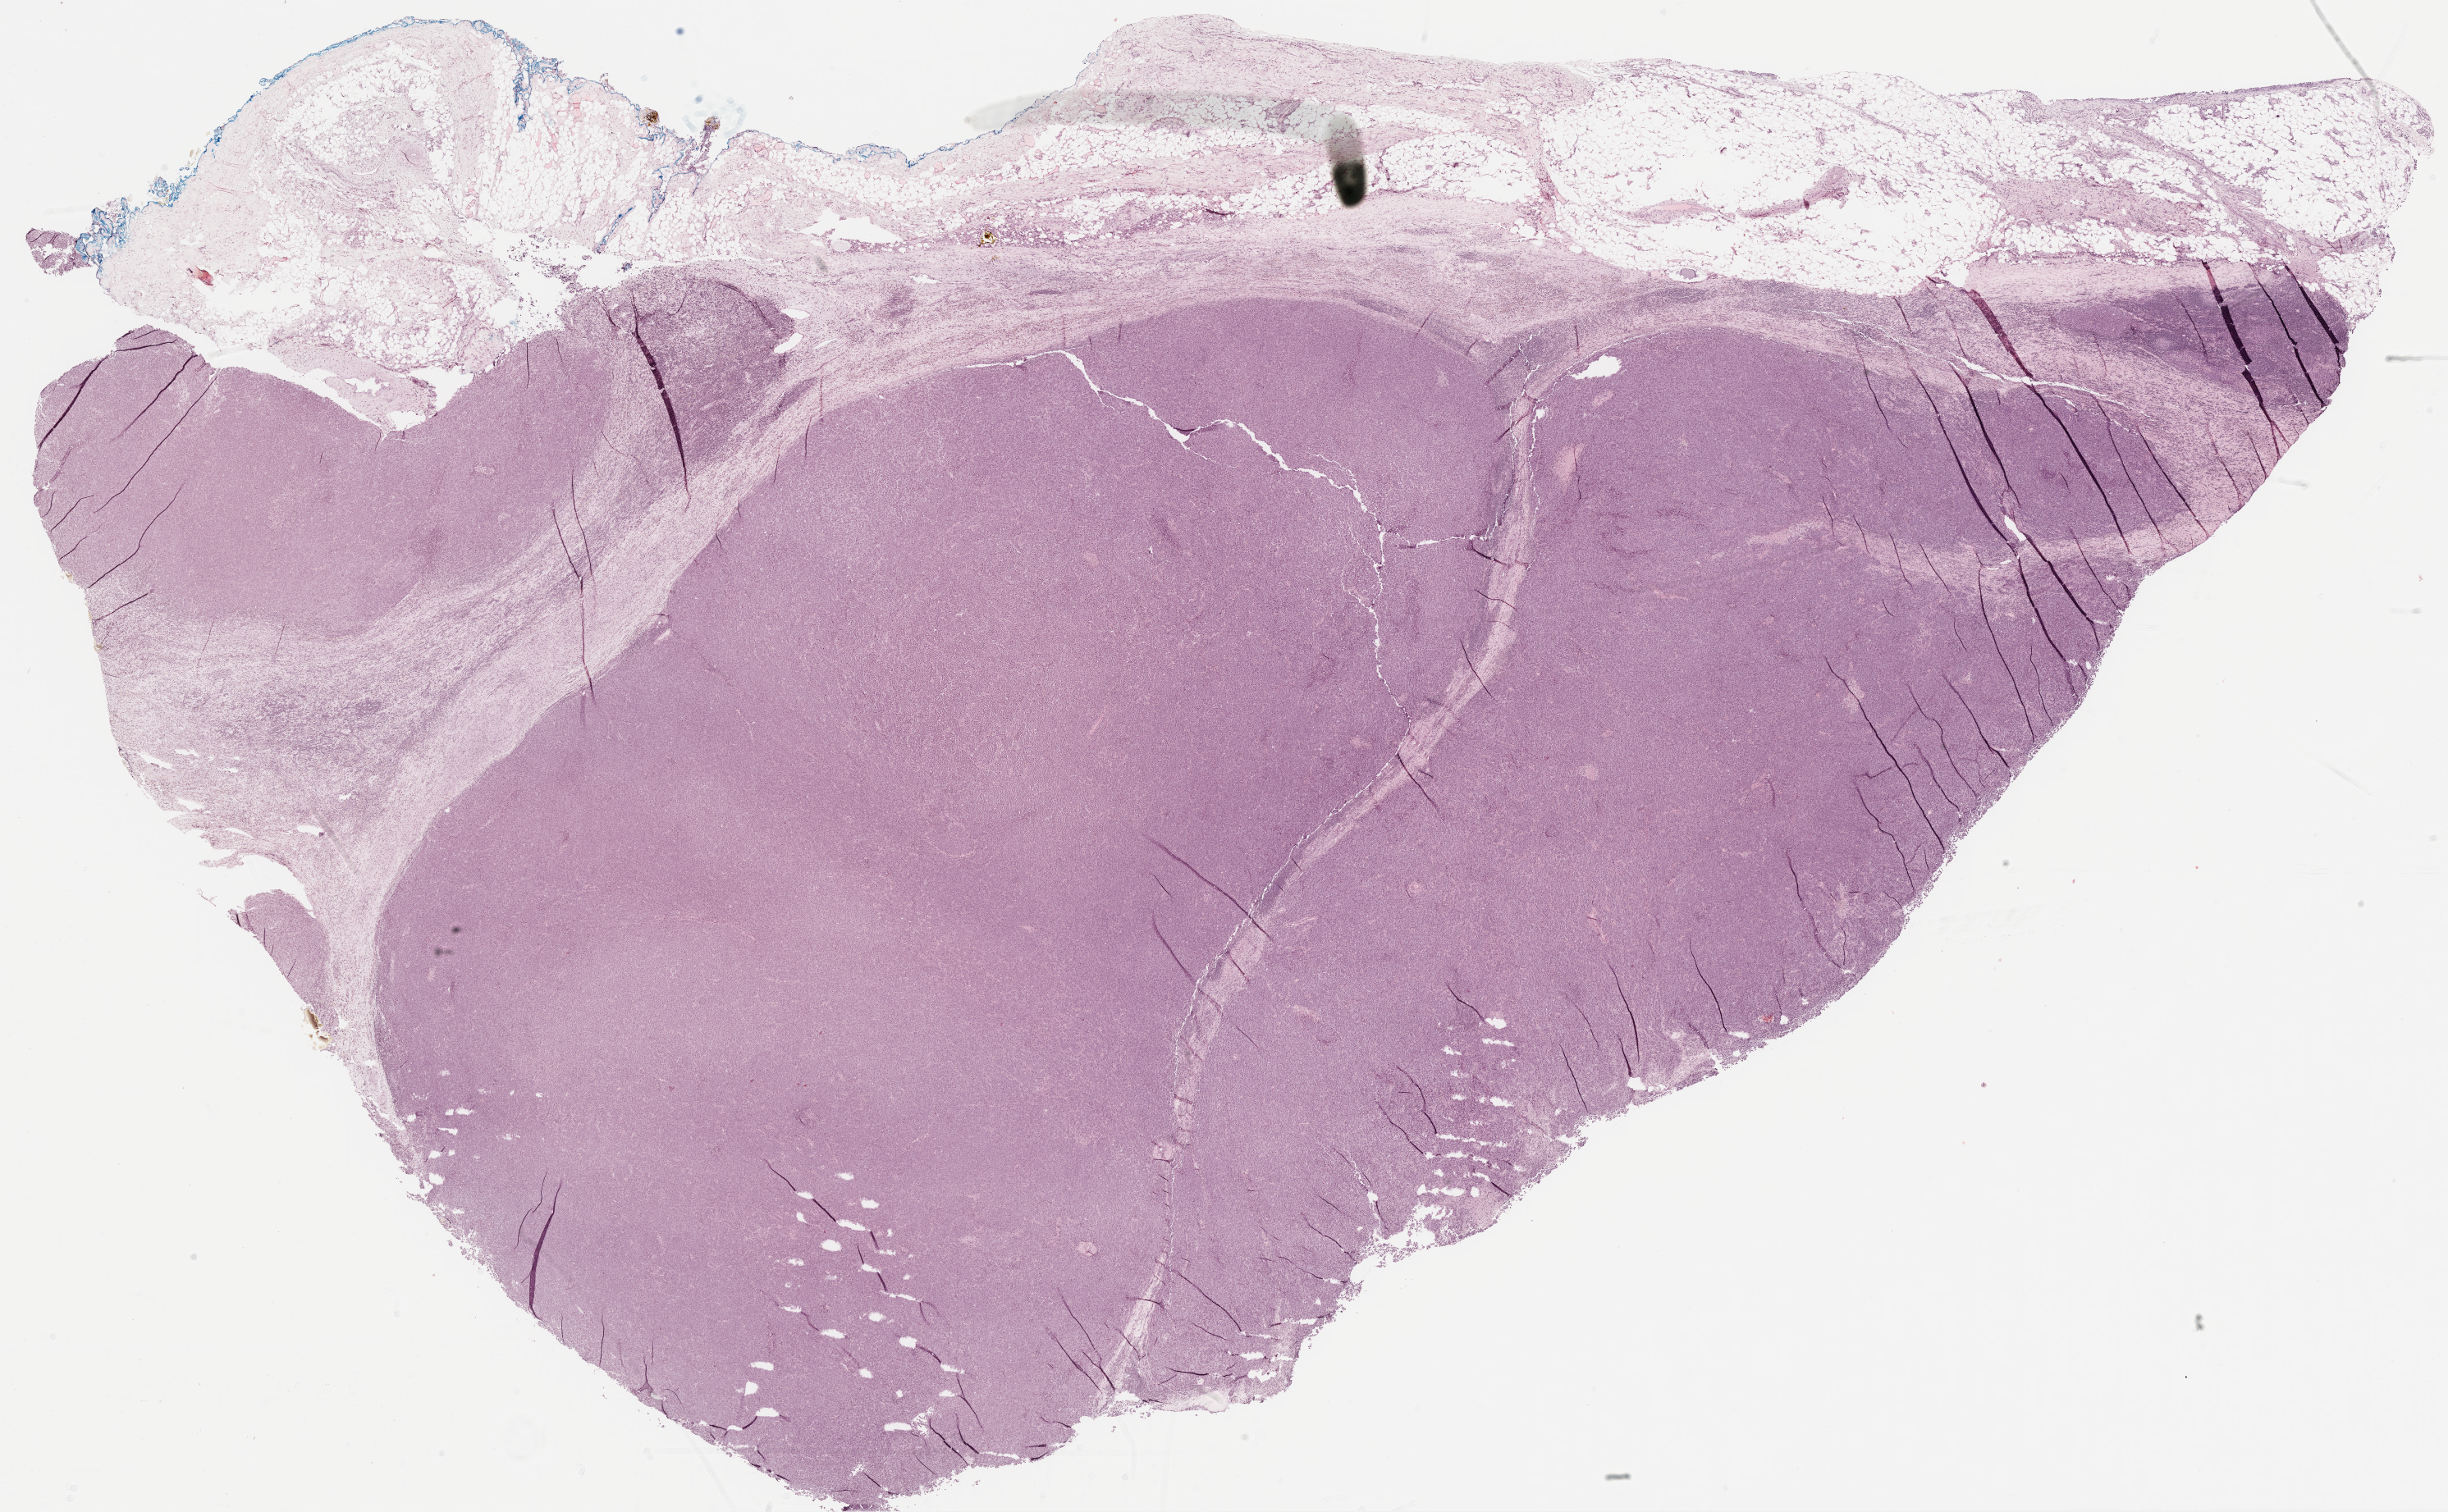
Digitized H&E tissue section (whole slide), shown as a low-resolution overview of the whole scanned area (about 24.1 x 14.9 mm), FFPE section, metastatic tumour sample. Female patient.
This section: metastatic tumour tissue. Patient diagnosis: Malignant melanoma, NOS.